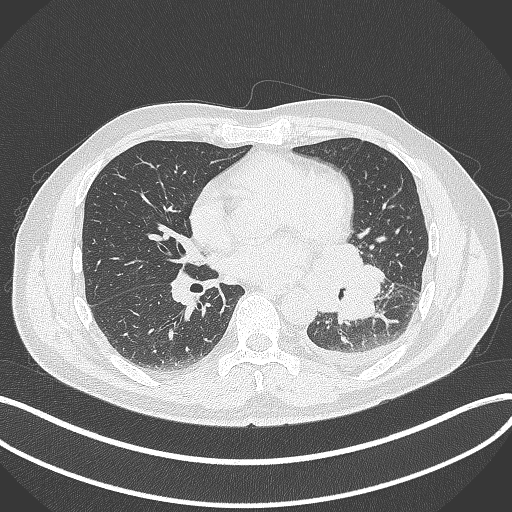
Chest CT, one axial slice. Slice 168 of 342 in the series (ordered by position). Reconstruction kernel B70f. 120 kVp. Lung window (W 1500 / L -600 HU). 1 mm slice thickness. 512 × 512 image matrix, field of view 400 × 400 mm. Patient: male, 58 years. From the clinical record (not read from this slice): clinical TNM (as recorded): T3 N1 M1b; histopathological grade: G3.
Outlined on this slice (bounding box drawn by a radiologist):
- lung tumour (recorded histology: small cell carcinoma): bounding box [x1, y1, x2, y2] px = [310, 236, 387, 331]